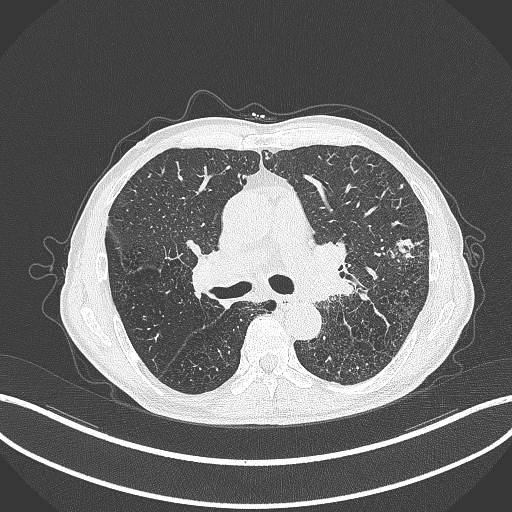
Chest CT, one axial slice. Reconstruction kernel B70f. Lung window (W 1500 / L -600 HU). 1 mm slice thickness. 512 × 512 image matrix. Patient: male, 74 years. From the clinical record (not read from this slice): clinical TNM (as recorded): T2a N1 M0.
Structures marked on this image (rectangle marked by the reading radiologist):
- lung tumour (recorded histology: adenocarcinoma): bounding box (x1, y1, x2, y2) in pixels: (394, 234, 421, 258)